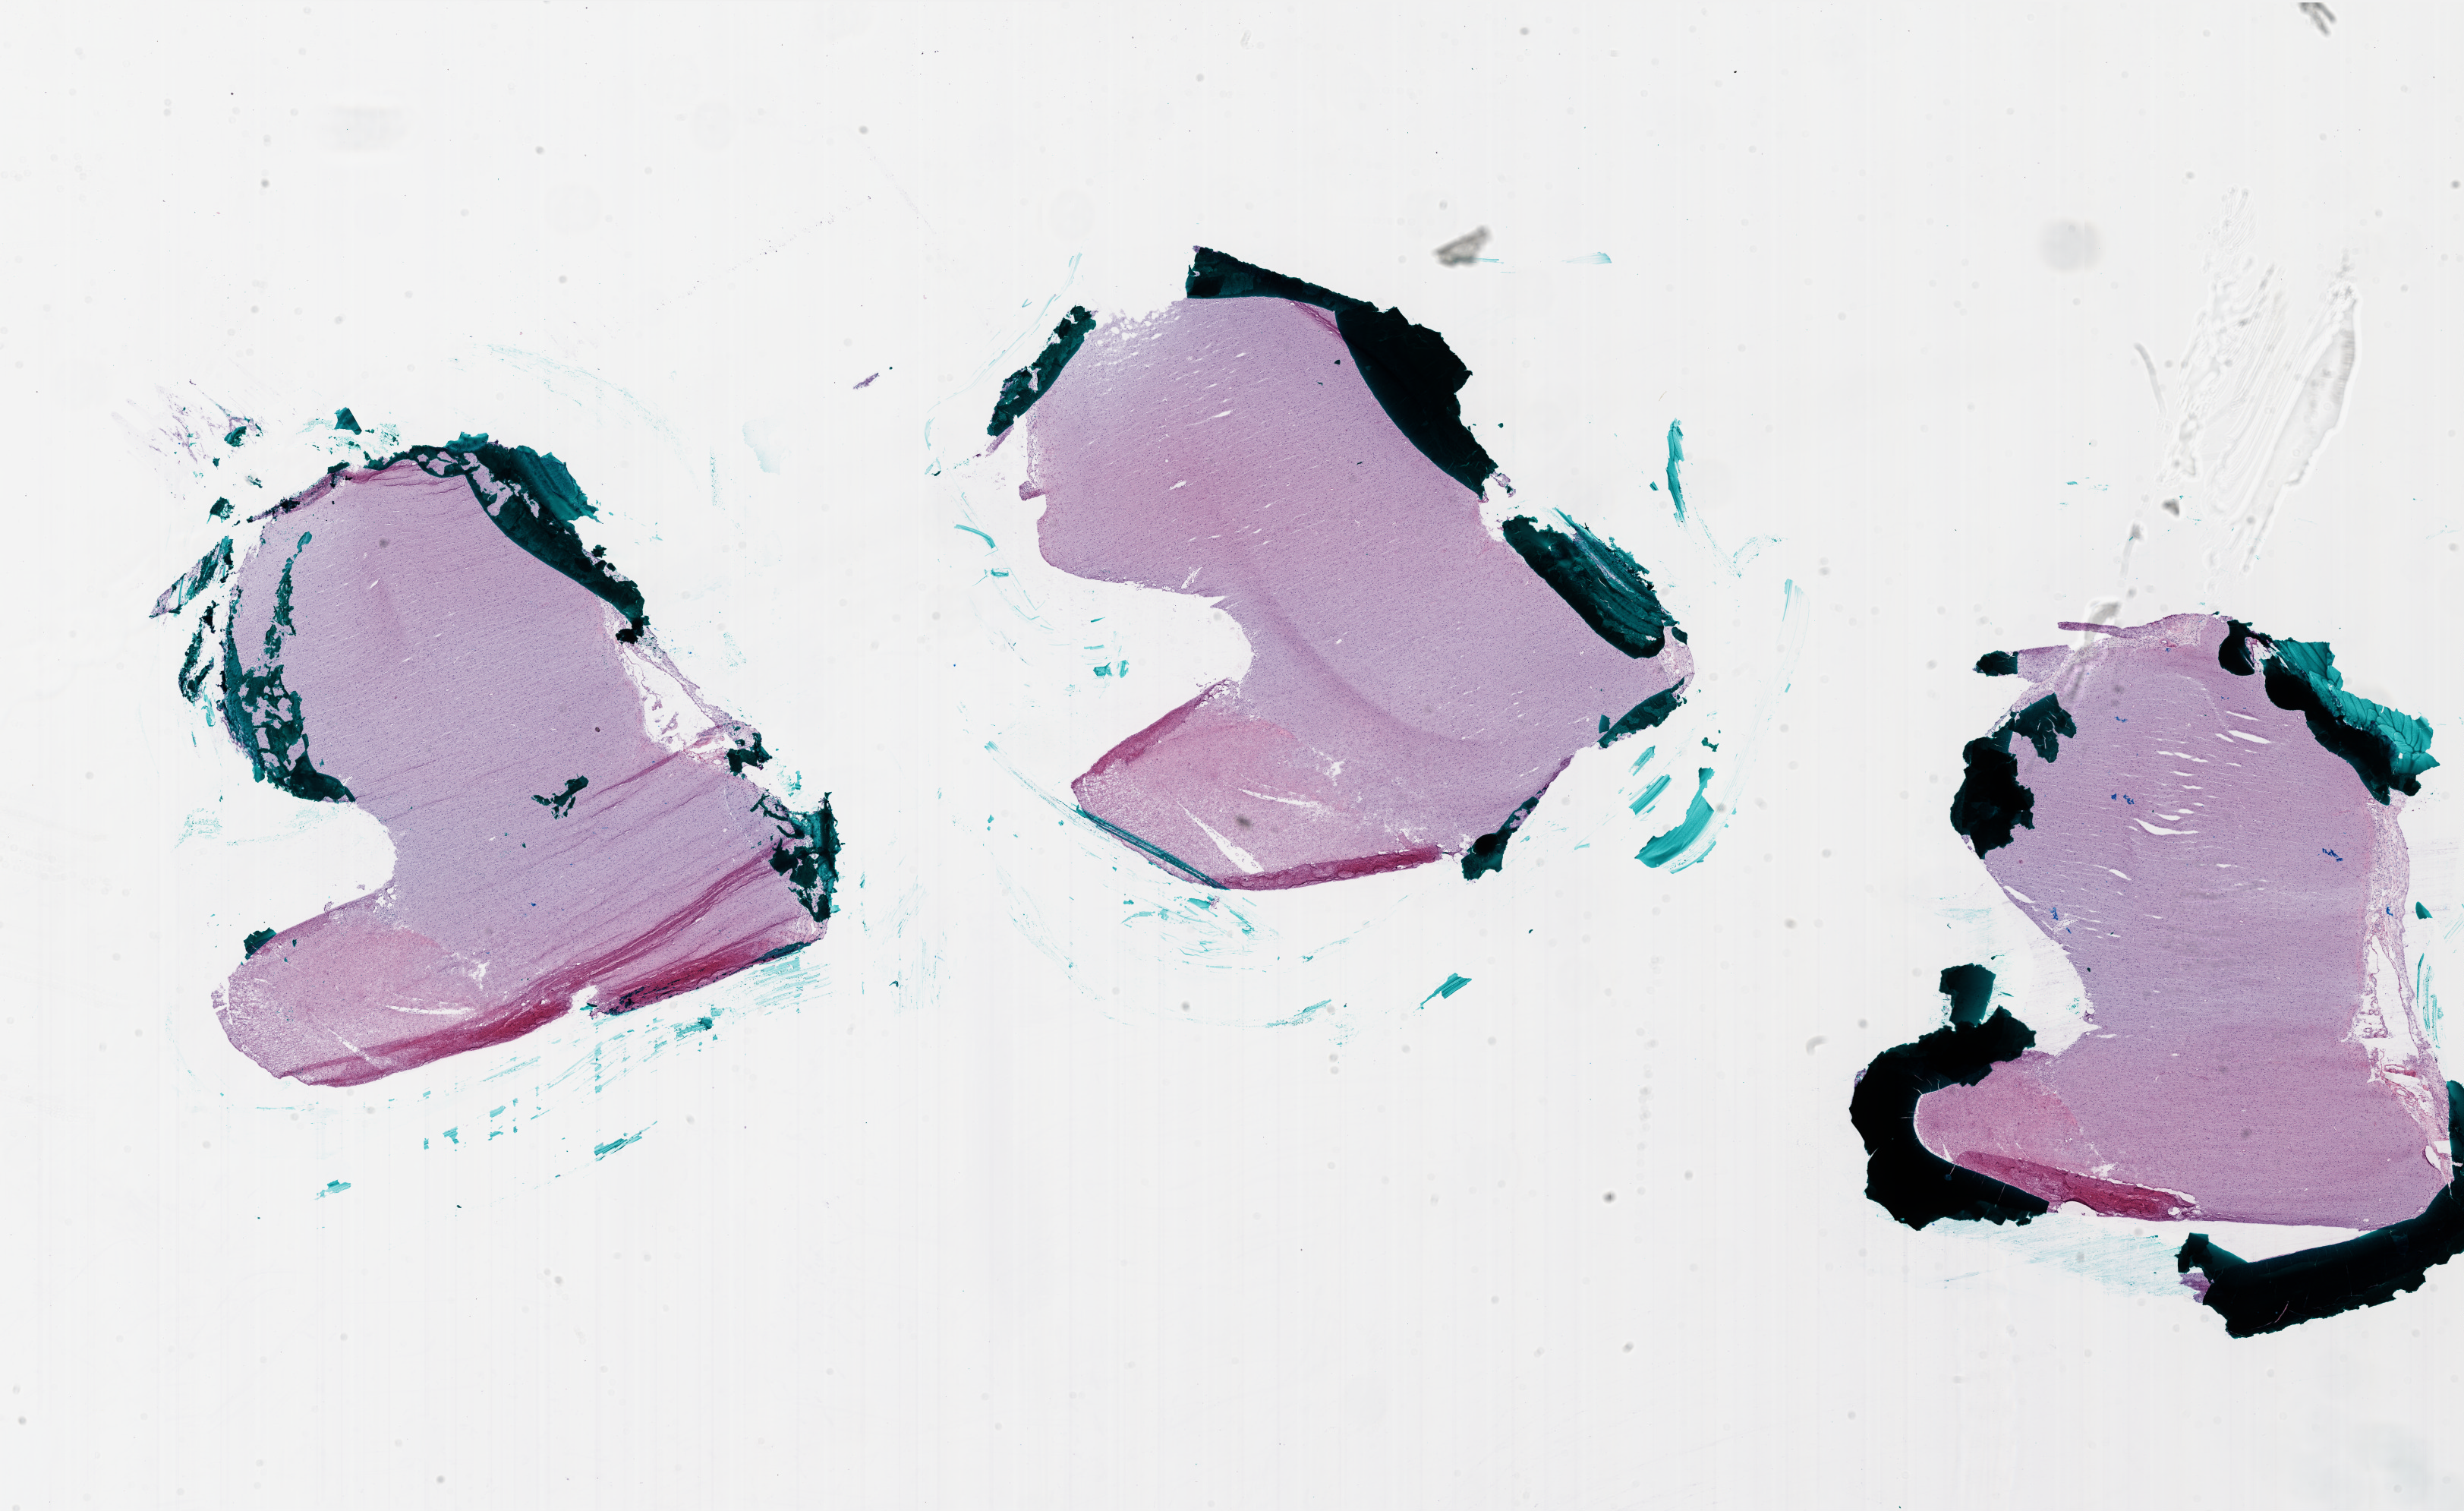
H&E-stained whole-slide image — low-resolution overview of the scanned area, about 26.0 x 15.9 mm (acquisition: 20x scan); frozen section; primary tumour sample from the brain. Patient: male, age at initial diagnosis 66 years. Pathologist review of this section (percent, as recorded): tumour cells 80%, tumour nuclei 95%.
Diagnosis: Glioblastoma.